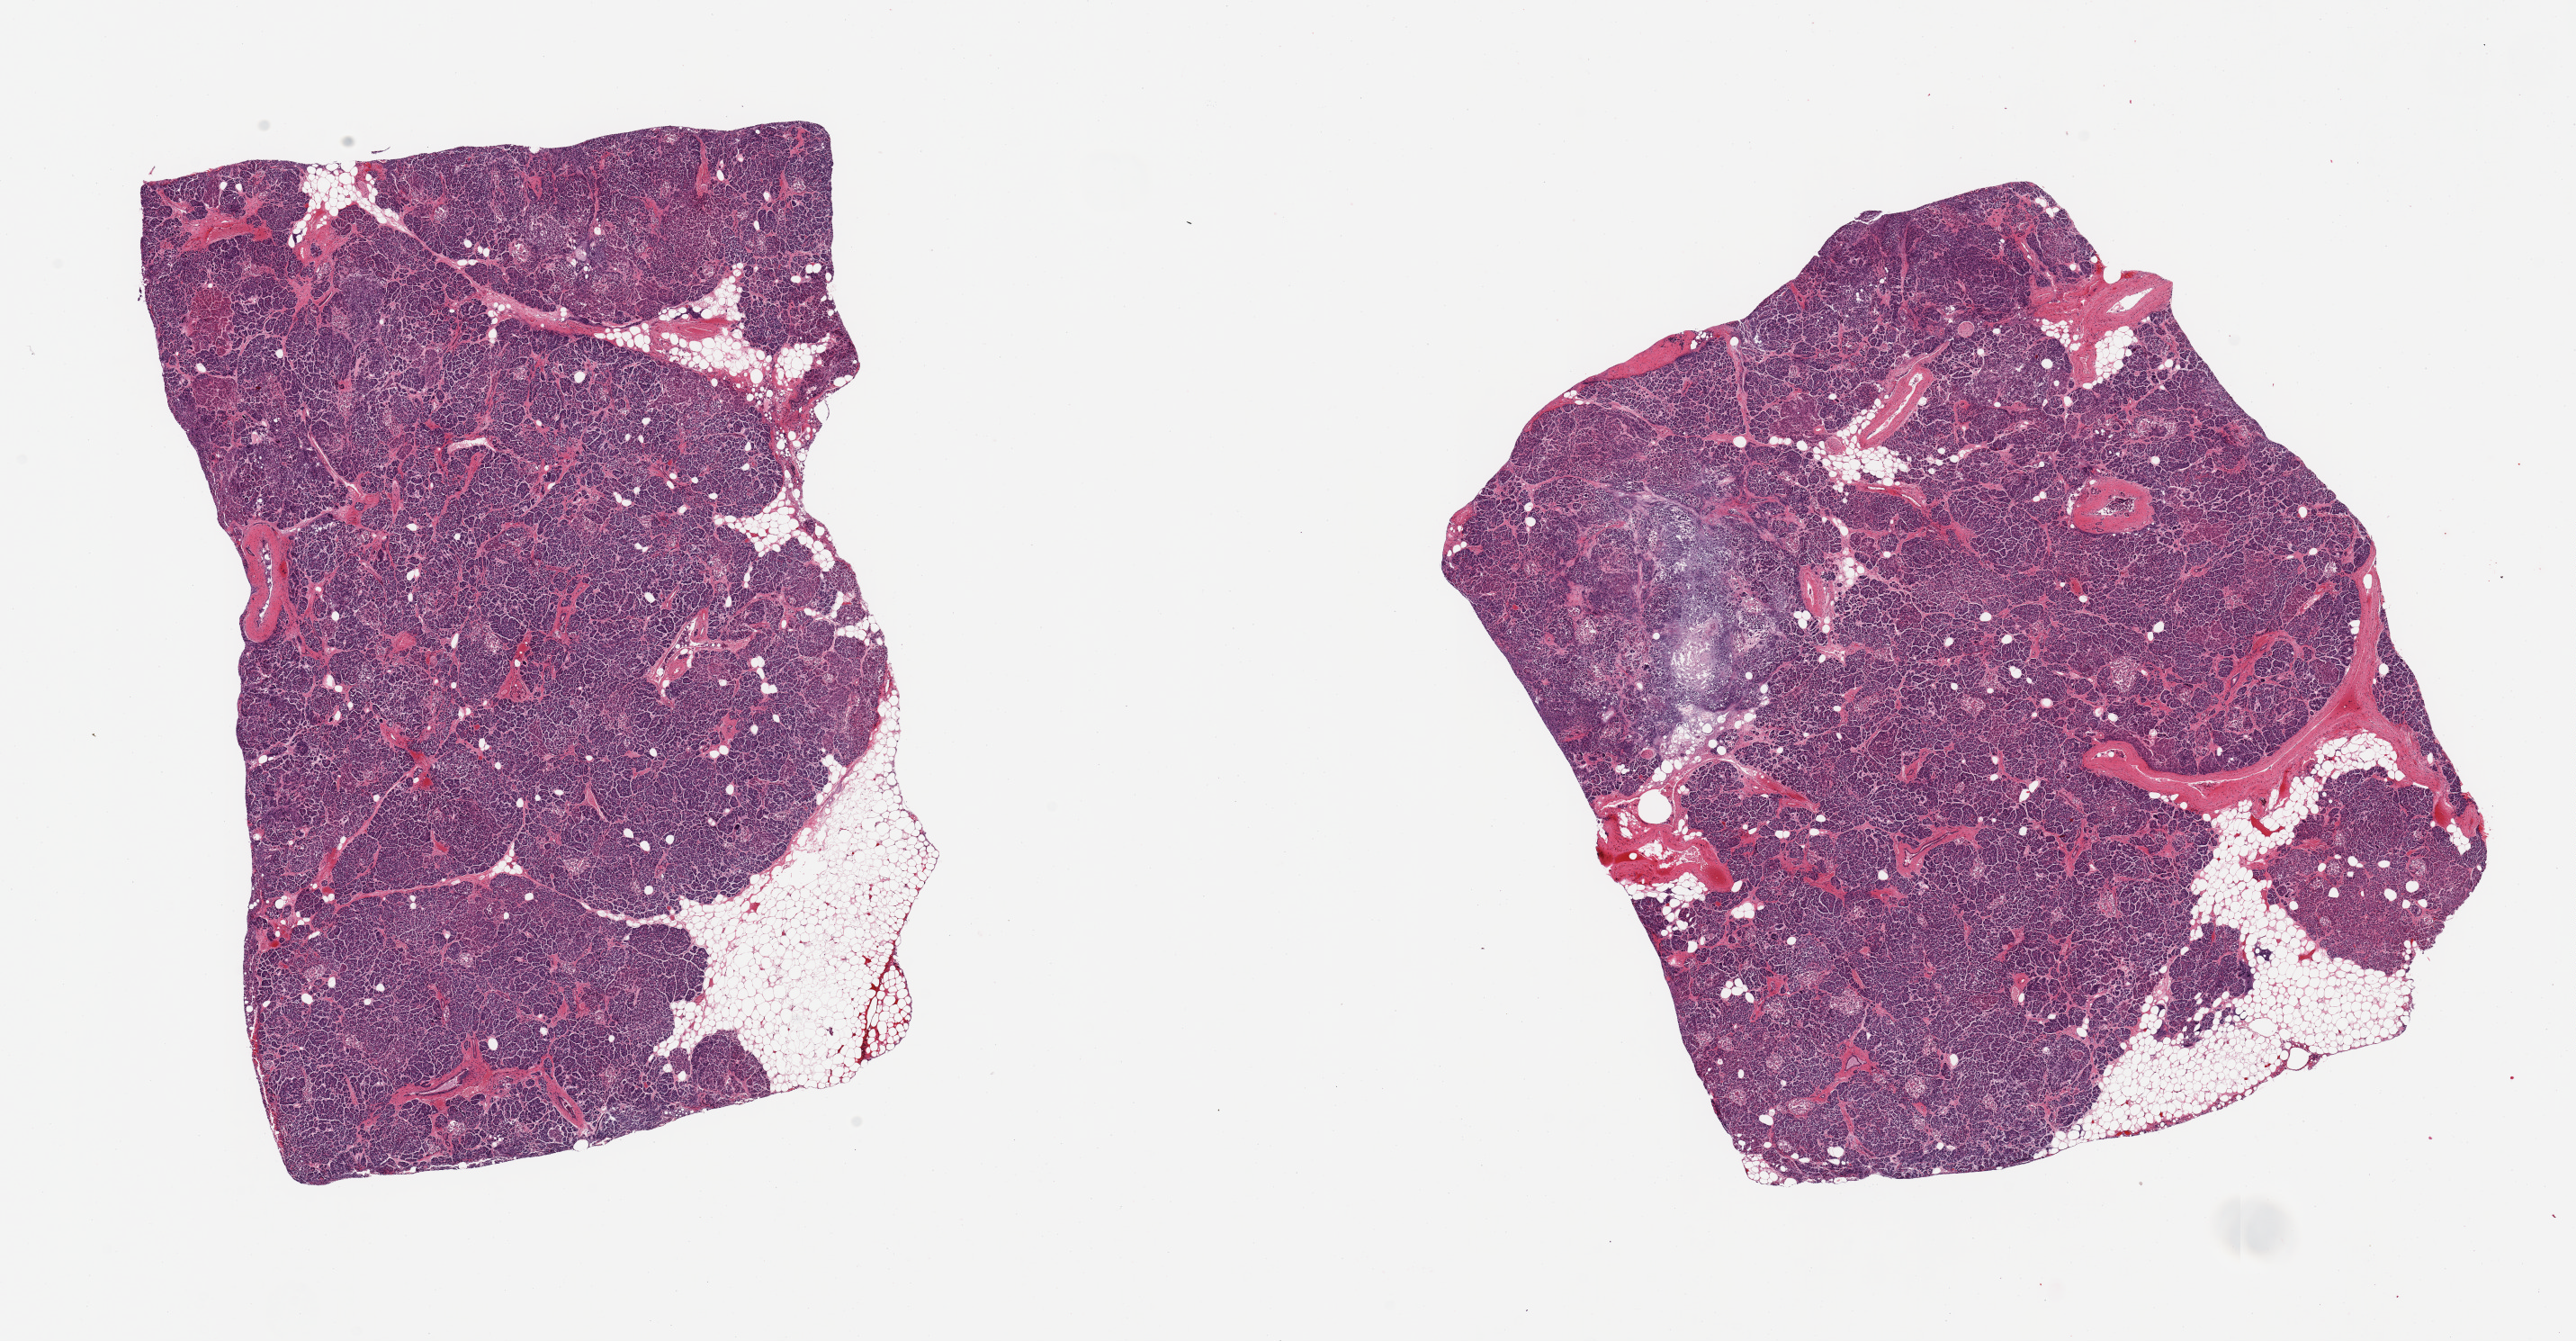
Whole-slide image, H&E stain, brightfield — a low-resolution overview of the entire scanned area, about 22.6 x 11.8 mm. PAXgene-fixed, paraffin-embedded tissue. Target tissue: pancreas. Tissue donor sample. Donor: male.
Pathologist's review note for this sample: 2 pieces; focal grade 3 autolysis; well preserved Langerhans islets; 10 - 15% internal fat.